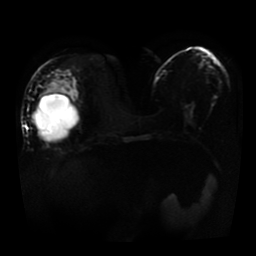
Breast MRI, one axial slice; position 14 of 41 along the scan axis; diffusion-weighted series; image 2 of 4 stored at this slice position (different b-values; order by instance number); 1.5 T; 5 mm slice thickness; 256 × 256 image matrix. Female patient.
Structures marked on this image (outlined manually by an expert reader):
- tumour on diffusion-weighted imaging: bounding box (x1, y1, x2, y2) in pixels: (47, 75, 75, 90)